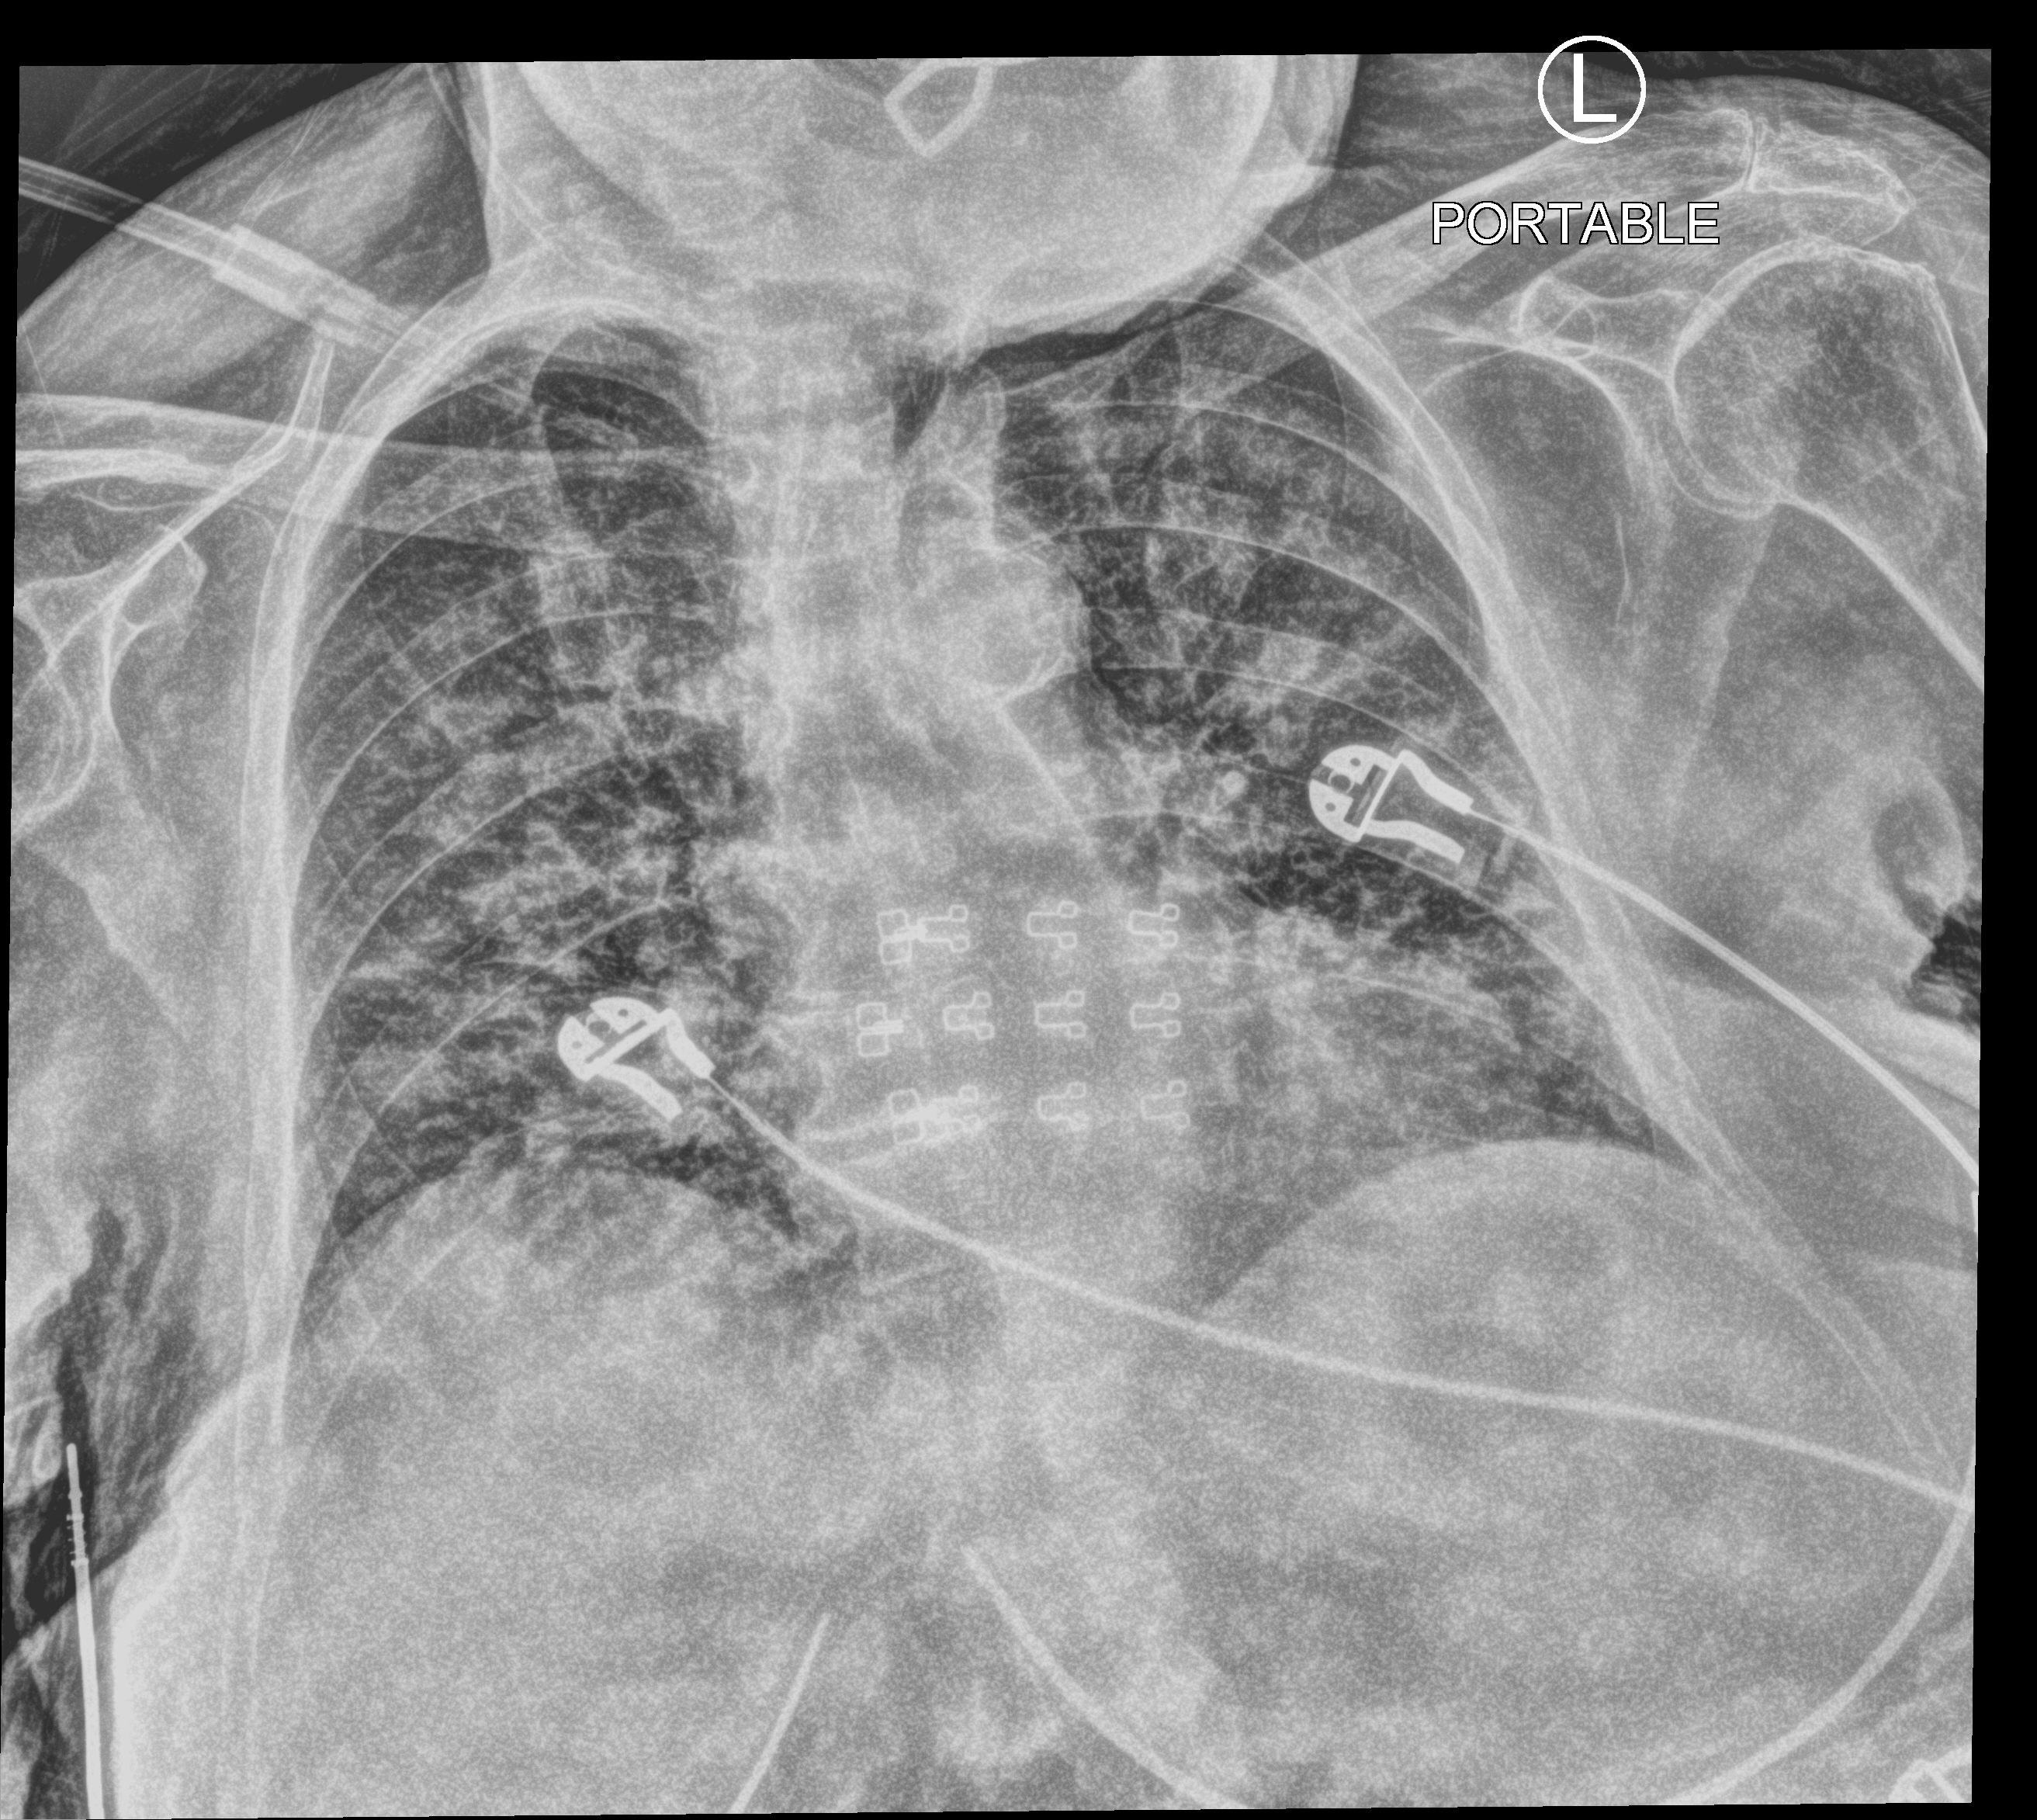
Chest X-ray (portable); anteroposterior (AP) projection. Female patient hospitalised with COVID-19, age 75–90 years.
Admission-level facts for this patient (not findings on this image; timing relative to this image not recorded): mechanically ventilated during this hospital stay: no.